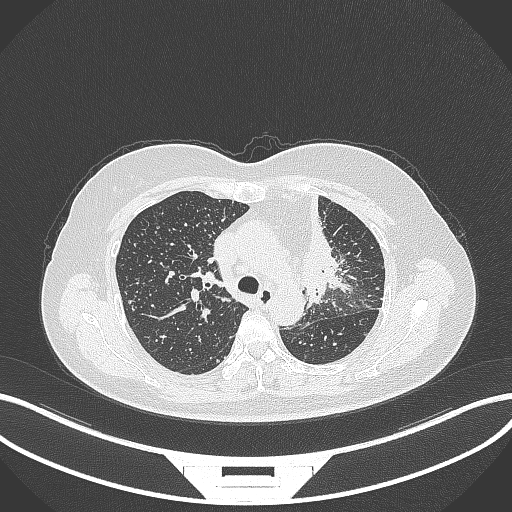
Chest CT, one axial slice. Slice 231 of 348 in the series (ordered by position). Reconstruction kernel B70f. 120 kVp. Lung window (W 1500 / L -600 HU). 512 × 512 image matrix, field of view 400 × 400 mm. Patient: female, 49 years. From the clinical record (not read from this slice): clinical TNM (as recorded): T1c N0 M1.
Outlined on this slice (bounding box drawn by a radiologist):
- lung tumour (recorded histology: adenocarcinoma): bounding box (x1, y1, x2, y2) in pixels: (286, 193, 351, 312)